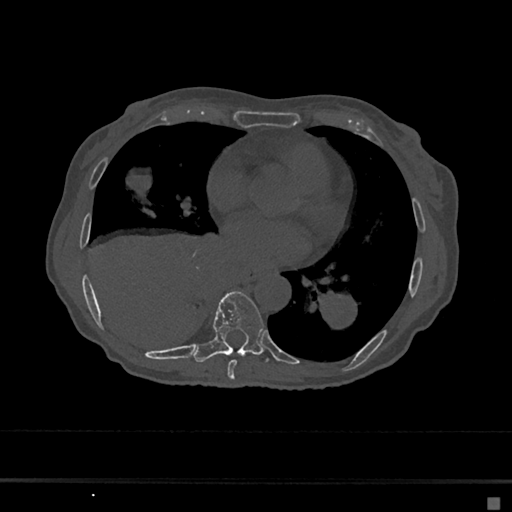
CT including the spine, one axial slice; slice 335 of 797 in the series (ordered by position); reconstruction kernel Br40s/3; 120 kVp; bone window (W 1800 / L 400 HU); 512 × 512 image matrix, field of view 360 × 360 mm. Female patient, age 68 years. Case-level facts recorded for this patient, not image findings: primary cancer: renal.
Structures marked on this image (semi-automatic segmentation, software-assisted and operator-edited):
- T7 vertebra: bounding box <227,360,237,380> (left, top, right, bottom; pixels)
- T8 vertebra: <193,291,268,363>